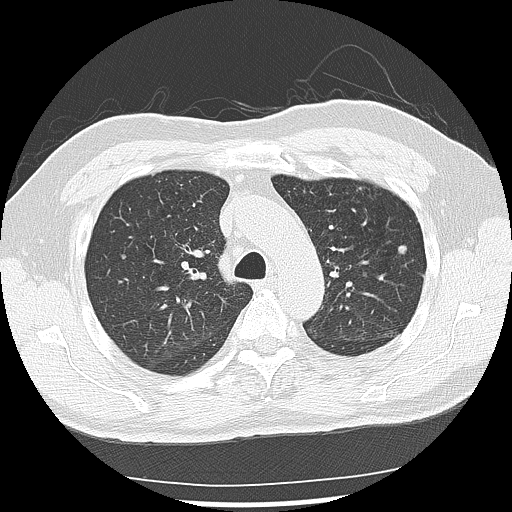
Low-dose screening chest CT, one axial slice. Slice 98 of 142 in the series (ordered by position). 120 kVp. Lung window (W 1500 / L -600 HU). 2.5 mm slice thickness. 512 × 512 image matrix.
Annotated regions visible in this slice (manually delineated by an expert):
- lesion 4 (nodule, upper lobe of left lung): bounding box (x1, y1, x2, y2) in pixels: (398, 245, 407, 255)